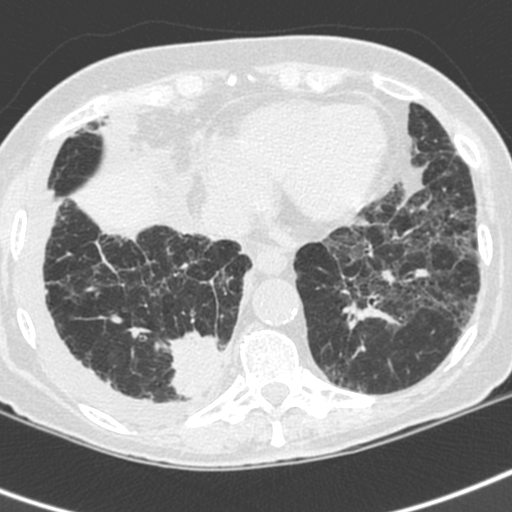
Chest CT (low-dose screening protocol), one axial image; baseline annual screen; lung window (W 1500 / L -600 HU); 1.3 mm slice thickness; standard (soft-tissue) reconstruction kernel (C); slice 140 of 192 in the series. Female, age 73 years at enrolment. Current smoker at enrolment.
Expert-annotated lung lesion, bounding box (x1, y1, x2, y2) in pixels: (156, 319, 234, 406). The exam's reader record, not a measurement of the box and not confirmed to be the same lesion: non-calcified nodule or mass ≥4 mm, right lower lobe, 35 × 30 mm, spiculated (stellate) margins, soft tissue attenuation. Participant outcome: lung cancer diagnosed 22 days after this screen — adenocarcinoma, NOS, right lower lobe, stage IV (AJCC 6th edition), 35 mm at pathology.